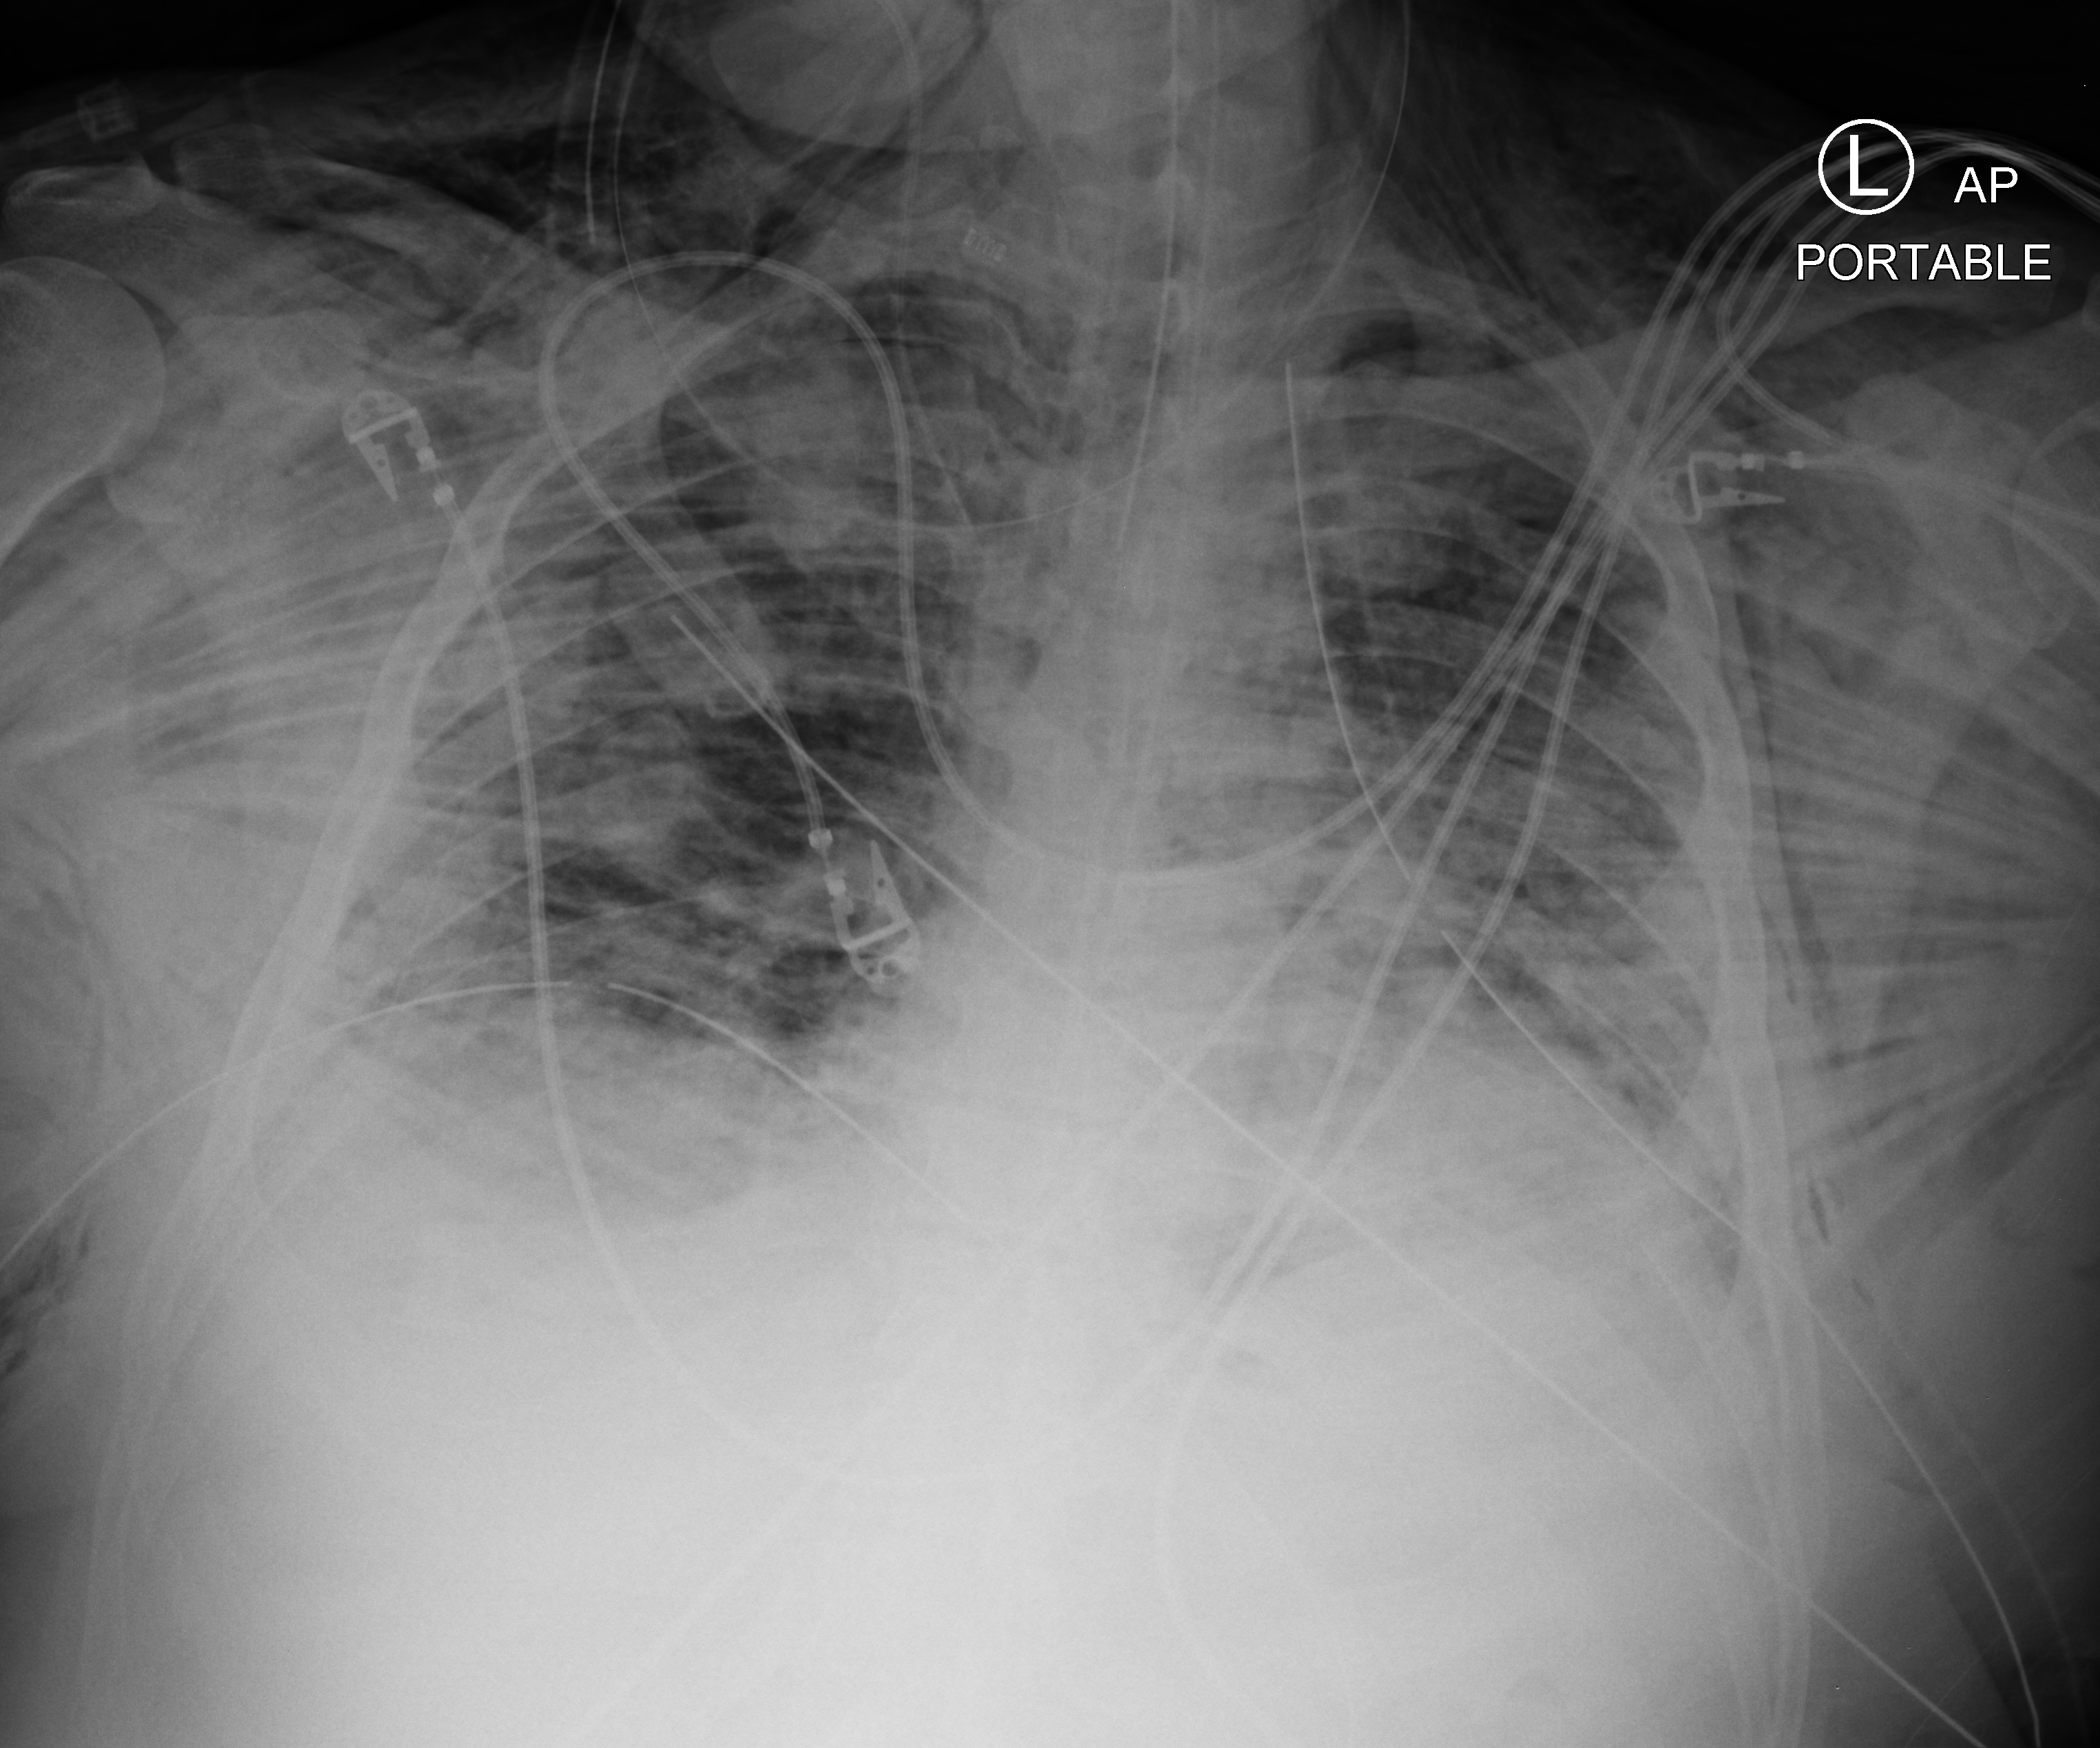
Portable chest radiograph. Patient hospitalised with COVID-19; male, aged 18–59 years.
Hospital-stay facts (about this admission, not read from this image; timing relative to this image not recorded):
- mechanically ventilated during this hospital stay: yes